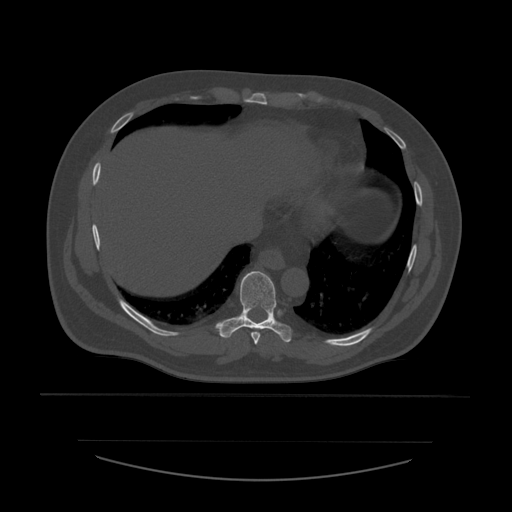
CT including the spine, one axial slice; slice 320 of 532 in the series (ordered by position); 120 kVp; bone window (W 1800 / L 400 HU); 512 × 512 image matrix, field of view 441 × 441 mm. Patient age 44 years. From the clinical record (not read from this slice): primary cancer: soft tissue sarcoma.
Annotated regions visible in this slice (semi-automatic segmentation, software-assisted and operator-edited):
- T8 vertebra: bounding box [x1, y1, x2, y2] px = [252, 332, 260, 345]
- T9 vertebra: [216, 271, 292, 343]